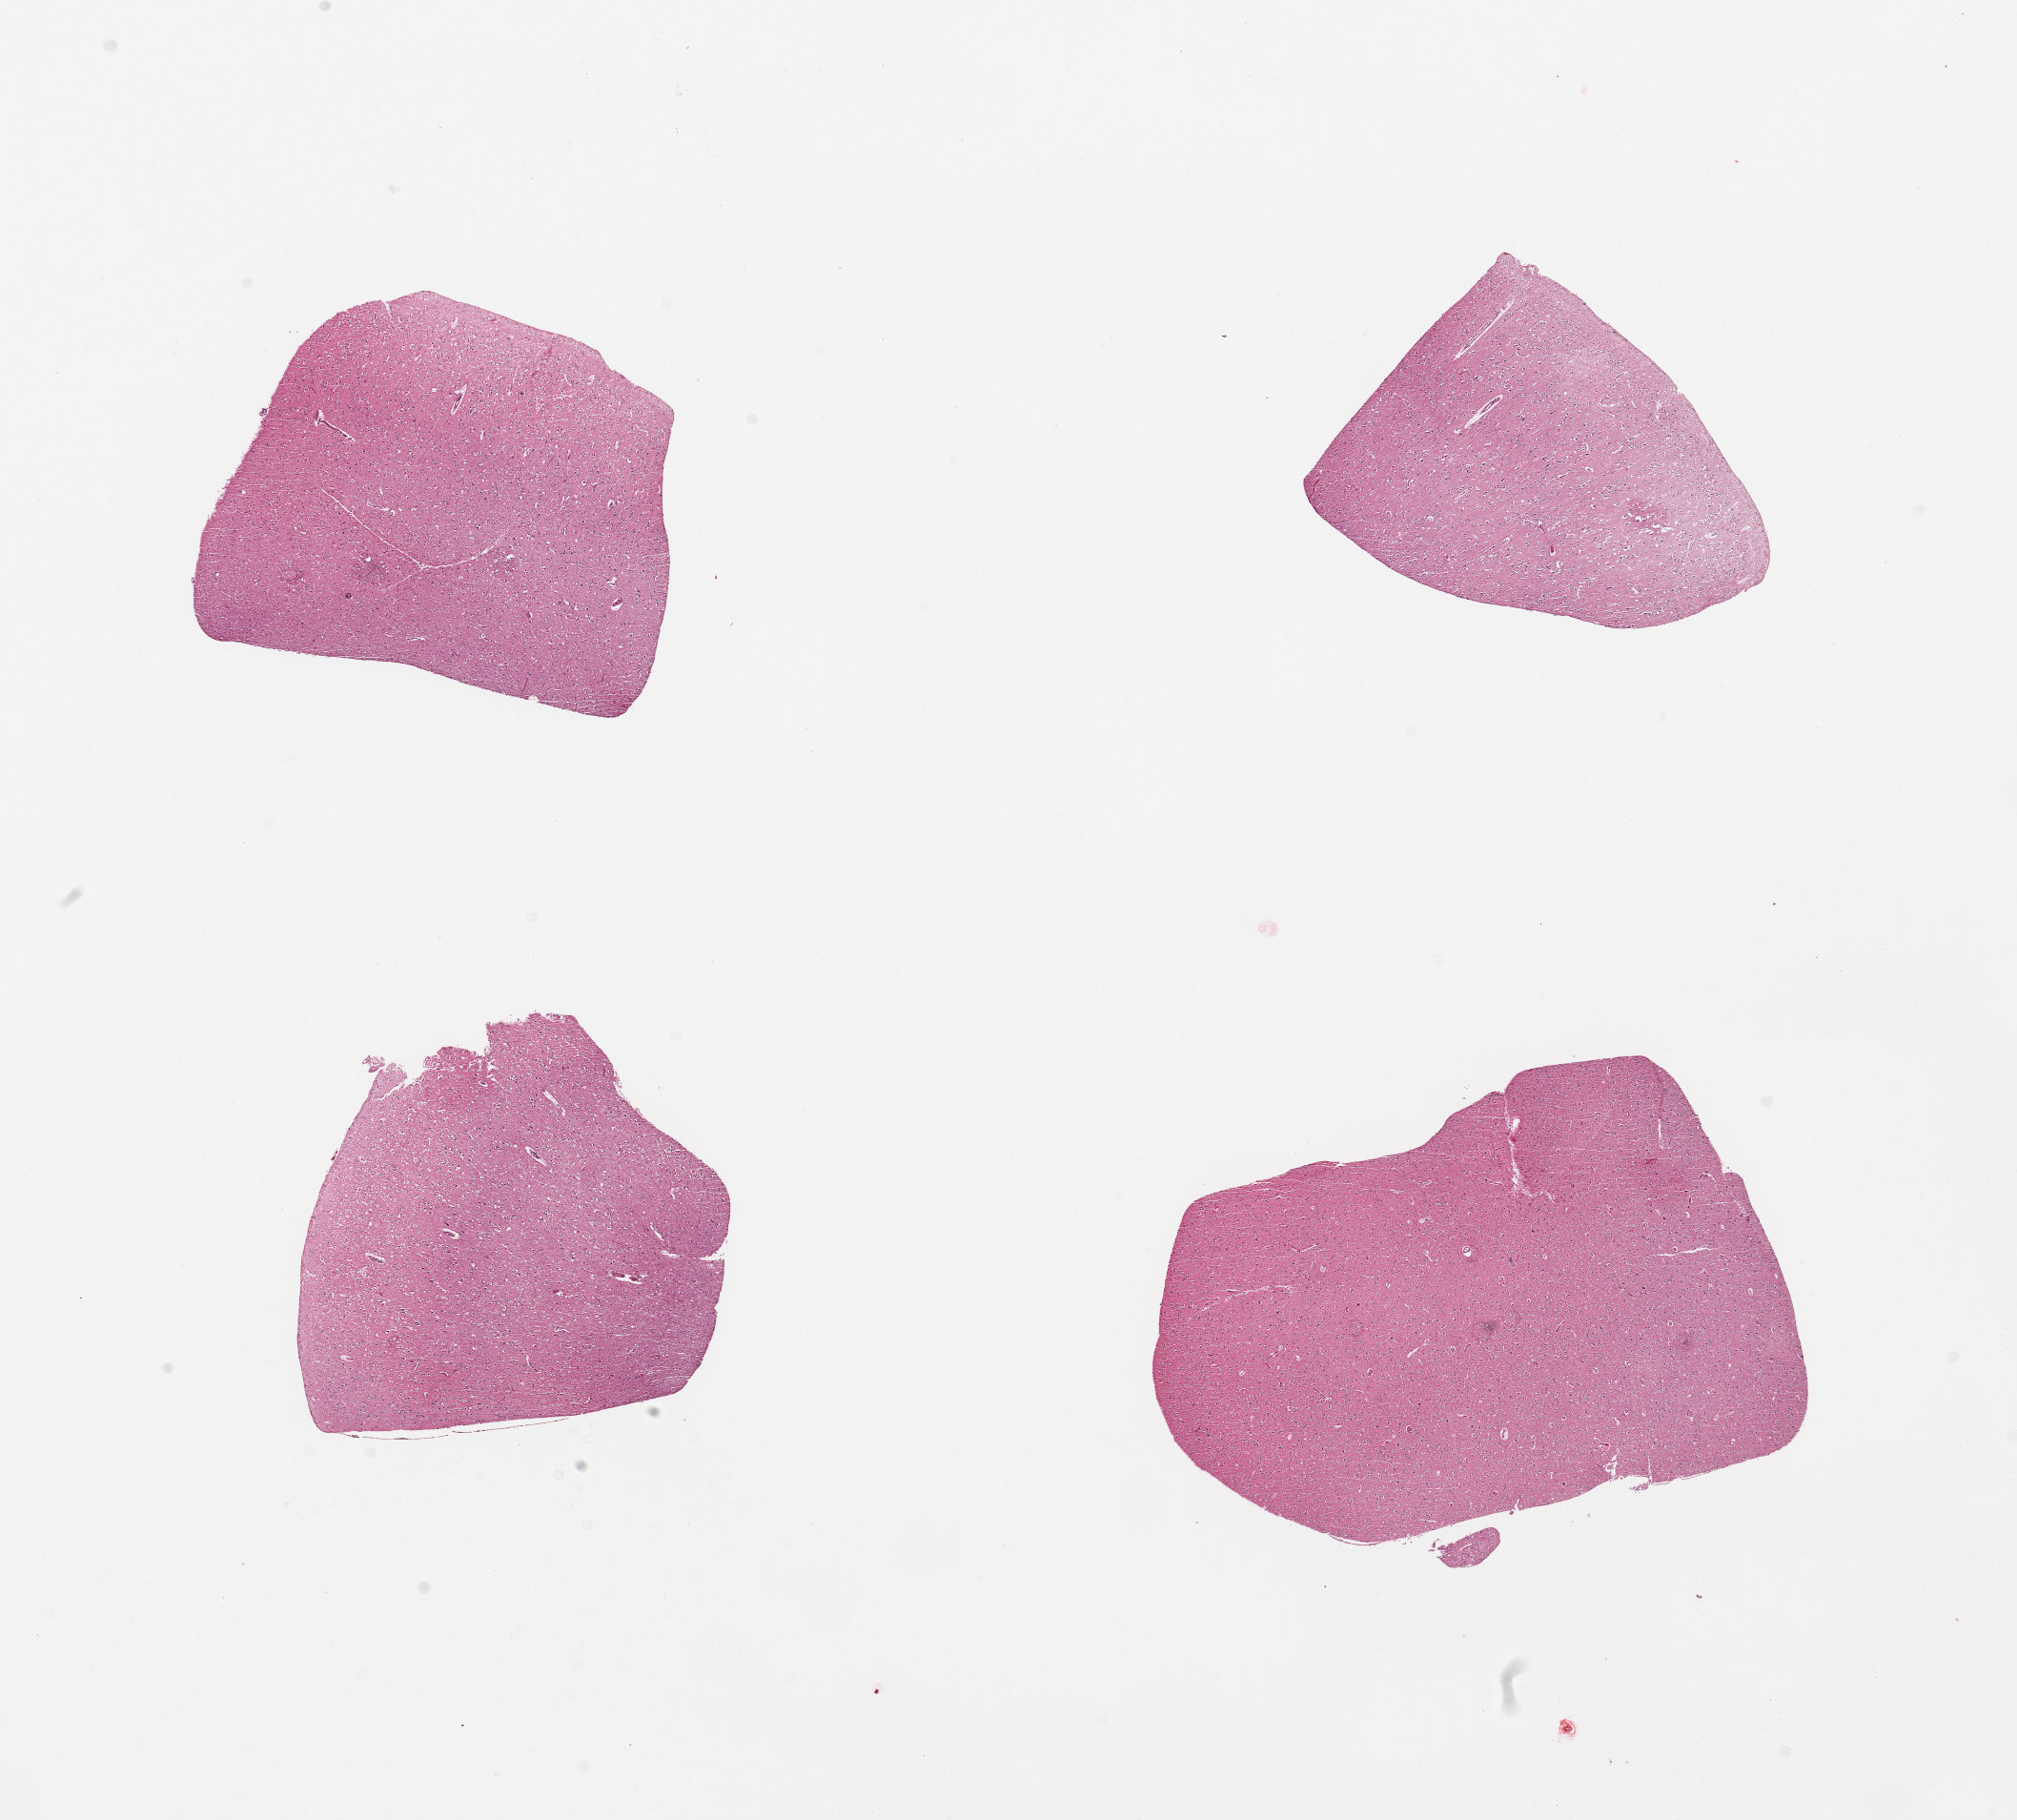
Whole-slide image, hematoxylin and eosin (H&E) stain, brightfield, whole scanned area (about 16.7 x 15.1 mm, from a 20x scan) shown as a low-resolution overview; PAXgene-fixed, paraffin-embedded tissue; sampled site (target tissue): cerebral cortex; donor tissue sample. Donor sex: female.
- review note (as recorded): 4 pieces of cerebrum